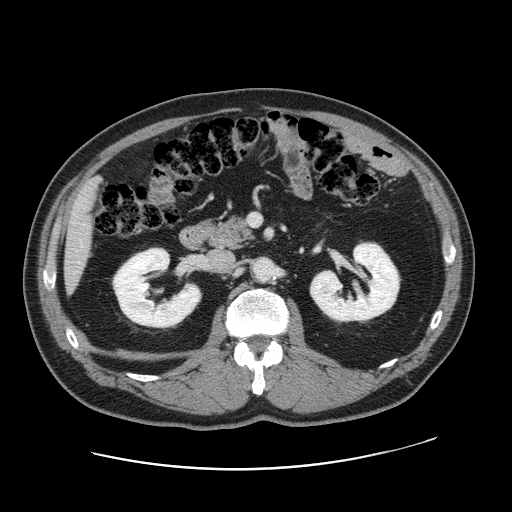
Contrast-enhanced abdominal CT, one axial slice. Slice 72 of 178 in the series (ordered by position). Intravenous contrast given. Soft-tissue window (W 400 / L 40 HU). 2.5 mm slice thickness. 512 × 512 image matrix. Male patient, age 63 years. Case-level facts recorded for this patient, not image findings: diagnosis: colorectal cancer liver metastases, imaged before liver resection; multiple liver metastases: yes.
Annotated regions visible in this slice (expert manual segmentation):
- liver: bounding box <65,183,97,286> (left, top, right, bottom; pixels)